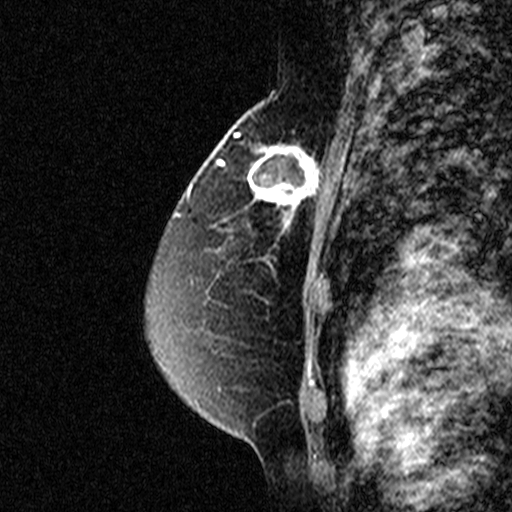
Breast MRI (dynamic contrast-enhanced), one sagittal slice. Position 28 of 44 along the scan axis. Dynamic contrast-enhanced study with each time point stored as its own series, time point 2 of 3 at this slice position (early post-contrast, ordered by acquisition time). 1.5 T. TE 4.5 ms, TR 11 ms. 3 mm slice thickness. 512 × 512 image matrix, field of view 200 × 200 mm. Patient: female, 49 years. Case-level facts recorded for this patient, not image findings: setting: breast cancer imaged before/during neoadjuvant chemotherapy; receptor status: triple-negative.
Structures marked on this image (semi-automatic segmentation, software-assisted and operator-edited):
- analysis volume of interest (the breast-tissue region the enhancement analysis was run in; not a lesion): bounding box (x1, y1, x2, y2) in pixels: (240, 122, 331, 227)
- tumour enhancement mask (voxels above the 90 % enhancement threshold inside the analysis volume of interest): (248, 144, 318, 225)